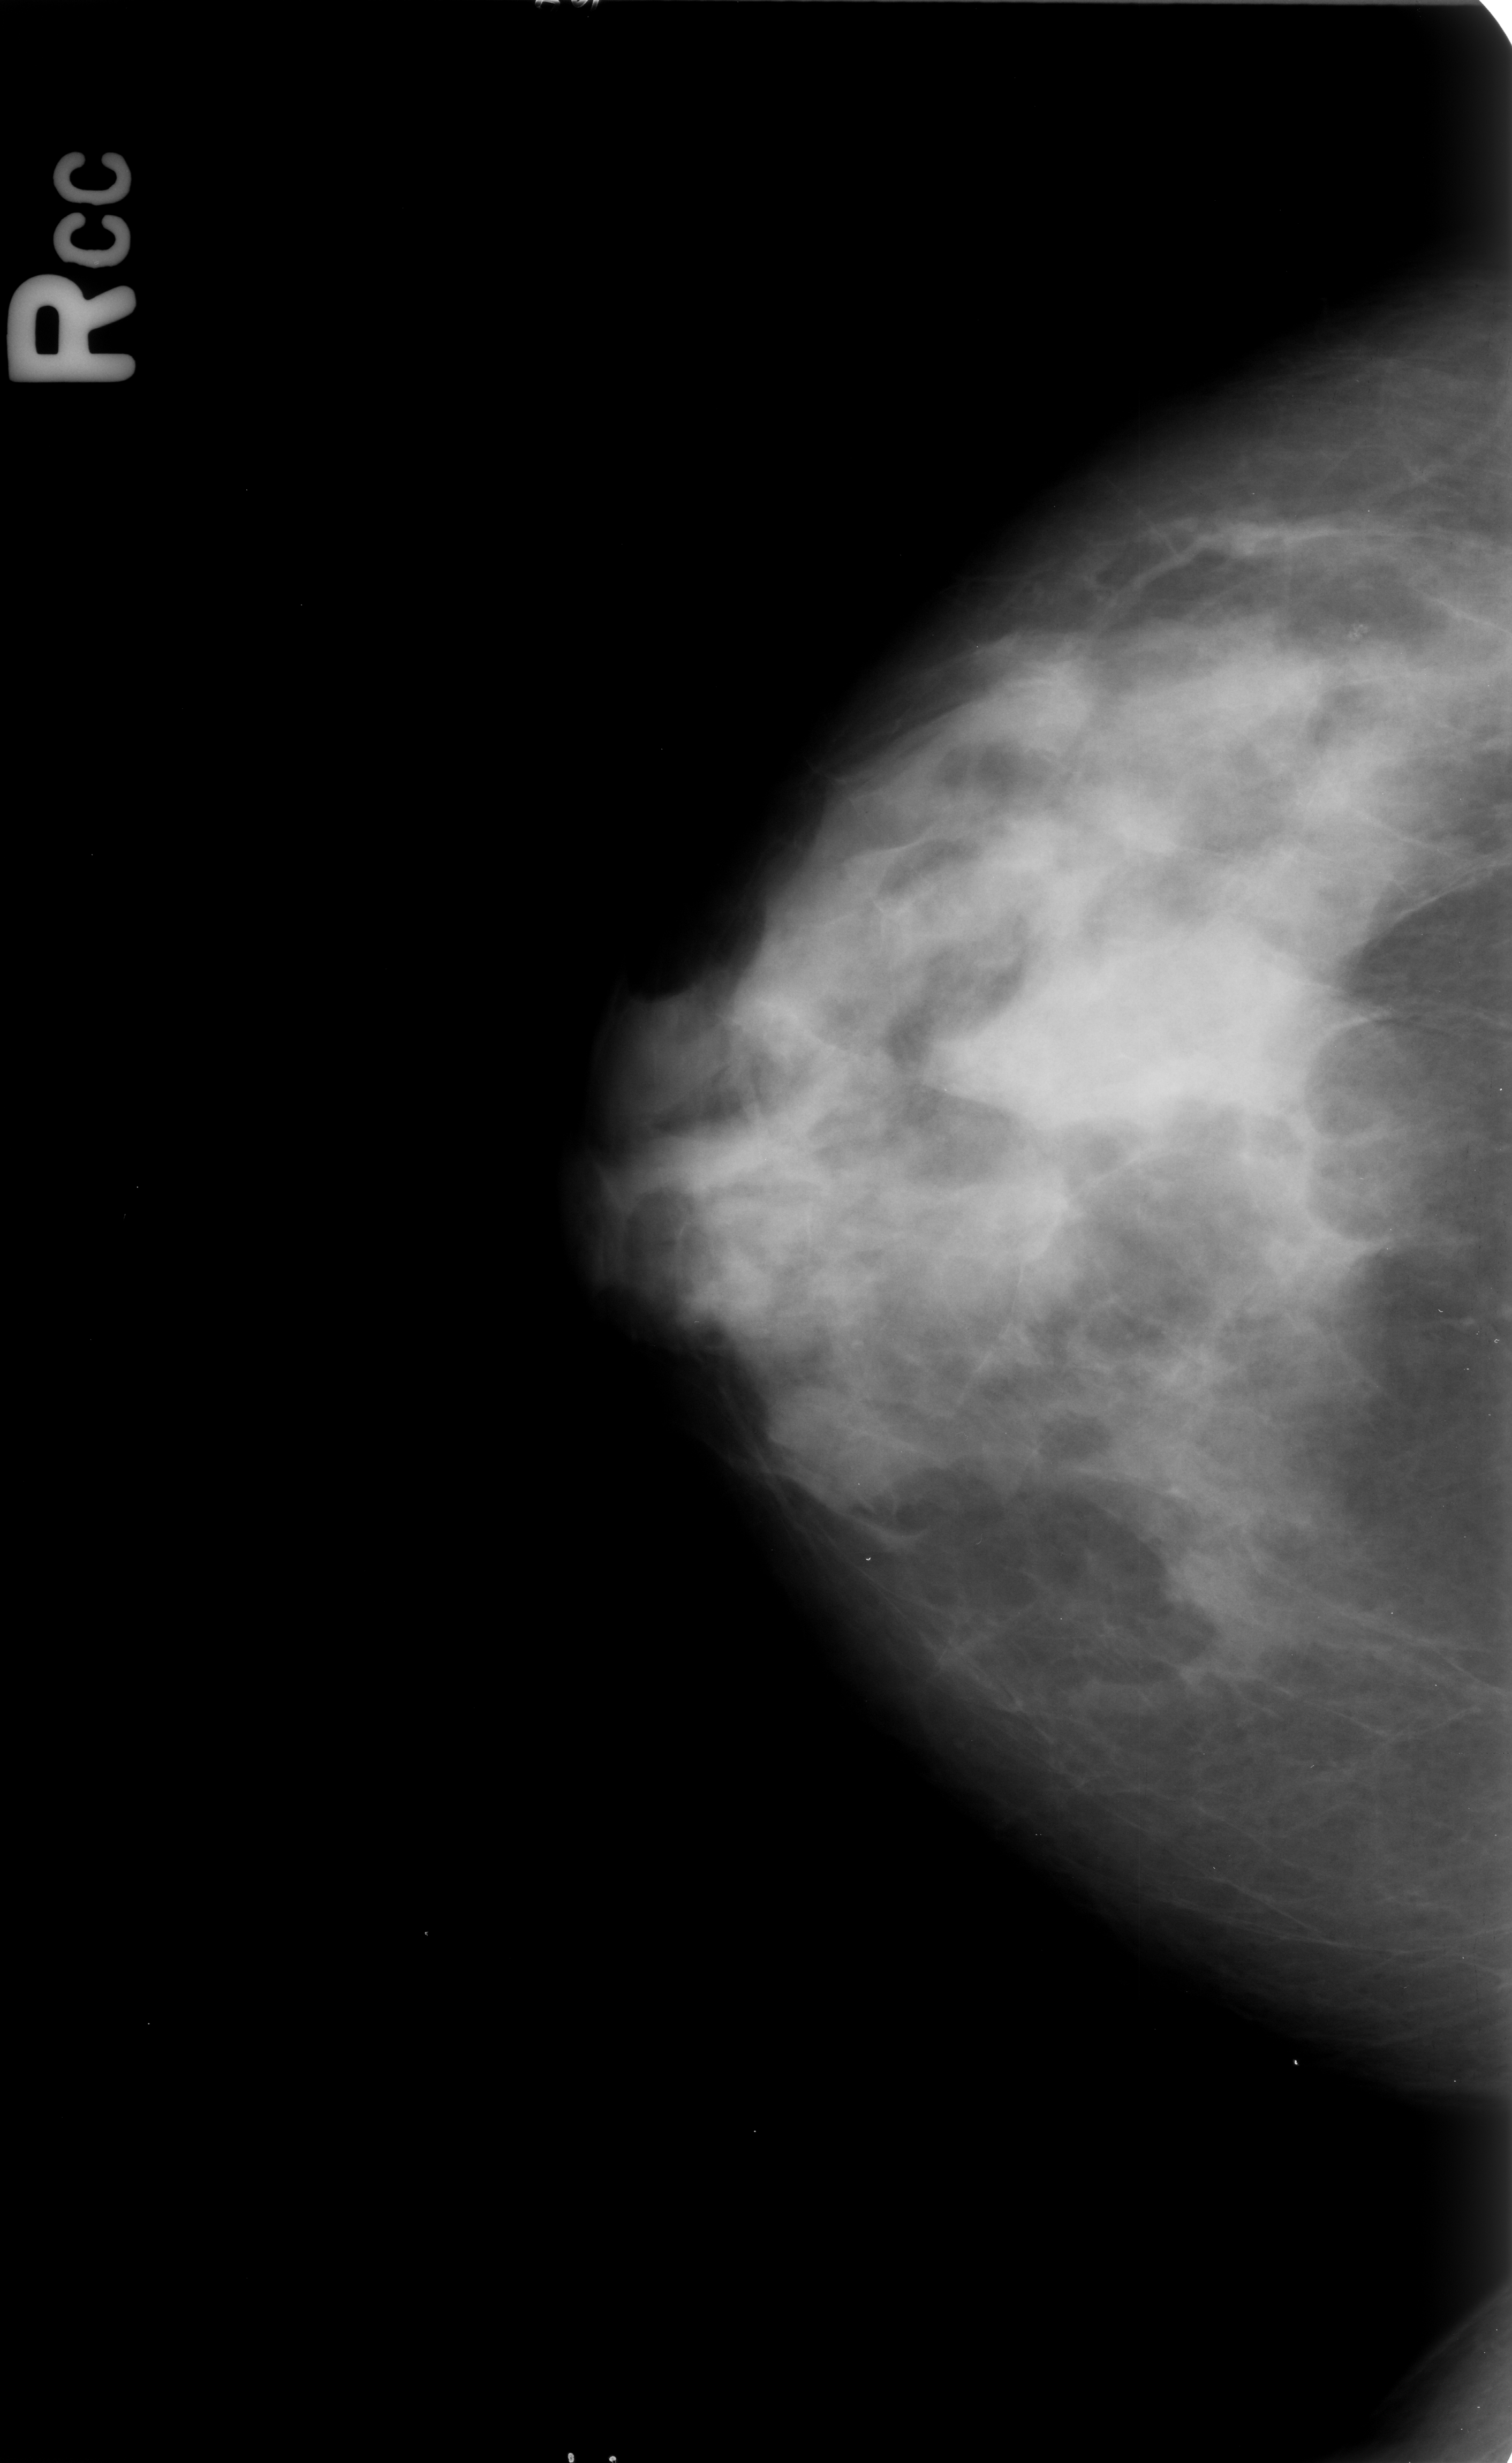
Digitized screen-film mammogram, right breast, CC view, BI-RADS breast density category 3 (scale 1–4).
Marked abnormality: calcifications, morphology amorphous / pleomorphic, distribution clustered; BI-RADS assessment category 4; pathology result (as recorded, not read from the image): benign.